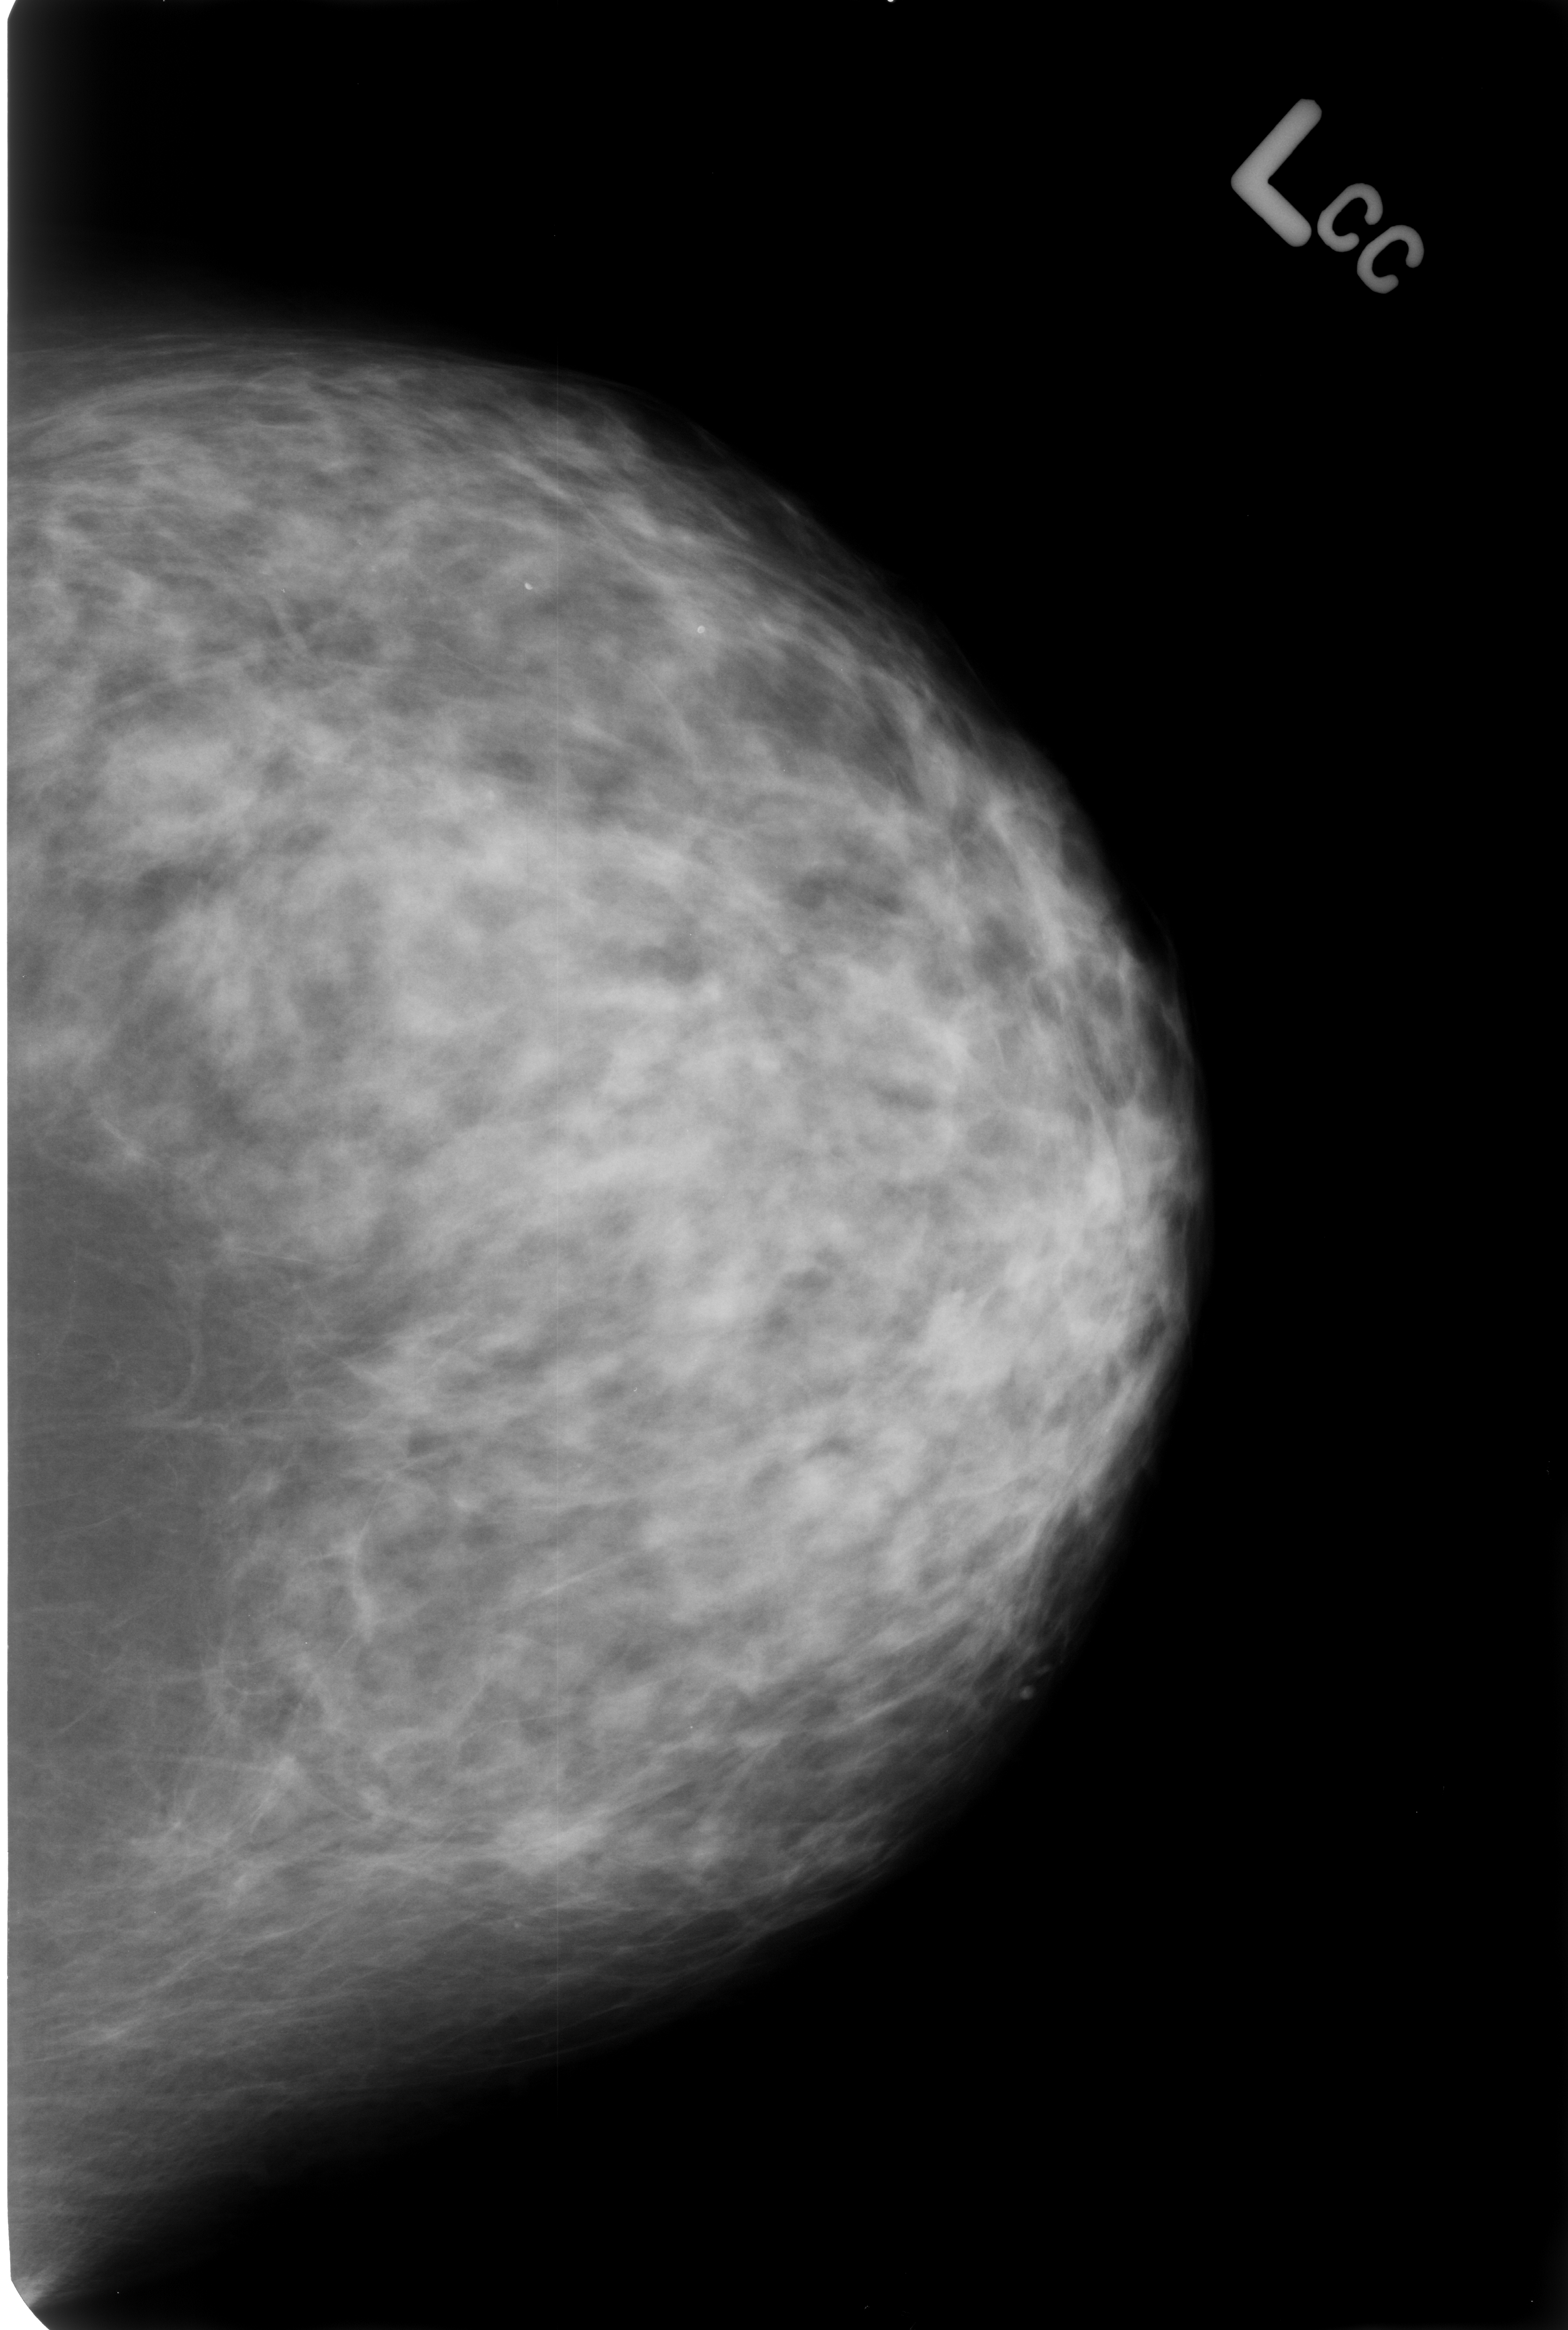
Digitized screen-film mammogram. Left breast. Craniocaudal (CC) view. Breast composition: heterogeneously dense (BI-RADS density category 3 of 4). 1568 × 2330 image matrix.
Expert-marked regions of interest on this image (one box per marked abnormality):
- Finding 1 of 2: calcifications, morphology lucent center; BI-RADS assessment category 2; subtlety rating 3 on a 1 (subtle) to 5 (obvious) scale; outcome (as recorded, no biopsy): benign without callback (not worked up further): box from (x=510, y=571) to (x=548, y=613) px
- Finding 2 of 2: calcifications, morphology lucent center; BI-RADS assessment category 2; benign; no additional work-up was recommended (outcome (as recorded, no biopsy): benign without callback): (x=684, y=615)–(x=718, y=645)